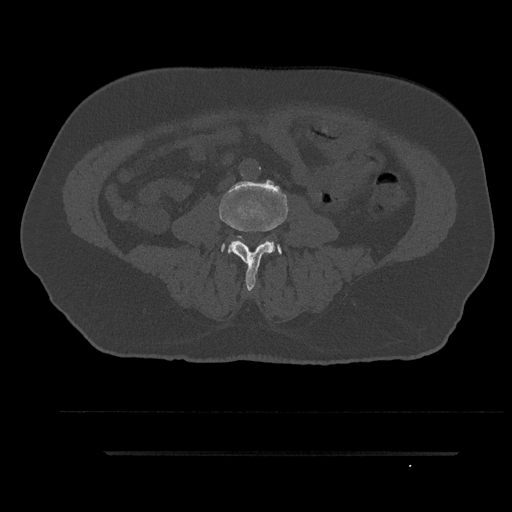
CT including the spine, one axial slice. Position 20 of 797 along the scan axis. Bone window (W 1800 / L 400 HU). 512 × 512 image matrix, field of view 432 × 432 mm. Patient: male, 63 years. From the clinical record (not read from this slice): primary cancer: renal; vertebrae with lytic lesions (as recorded): T8.
Annotated regions visible in this slice (semi-automatically segmented with operator editing):
- L3 vertebra: box from (x=219, y=185) to (x=288, y=292) px
- L4 vertebra: (x=221, y=241)–(x=282, y=255)